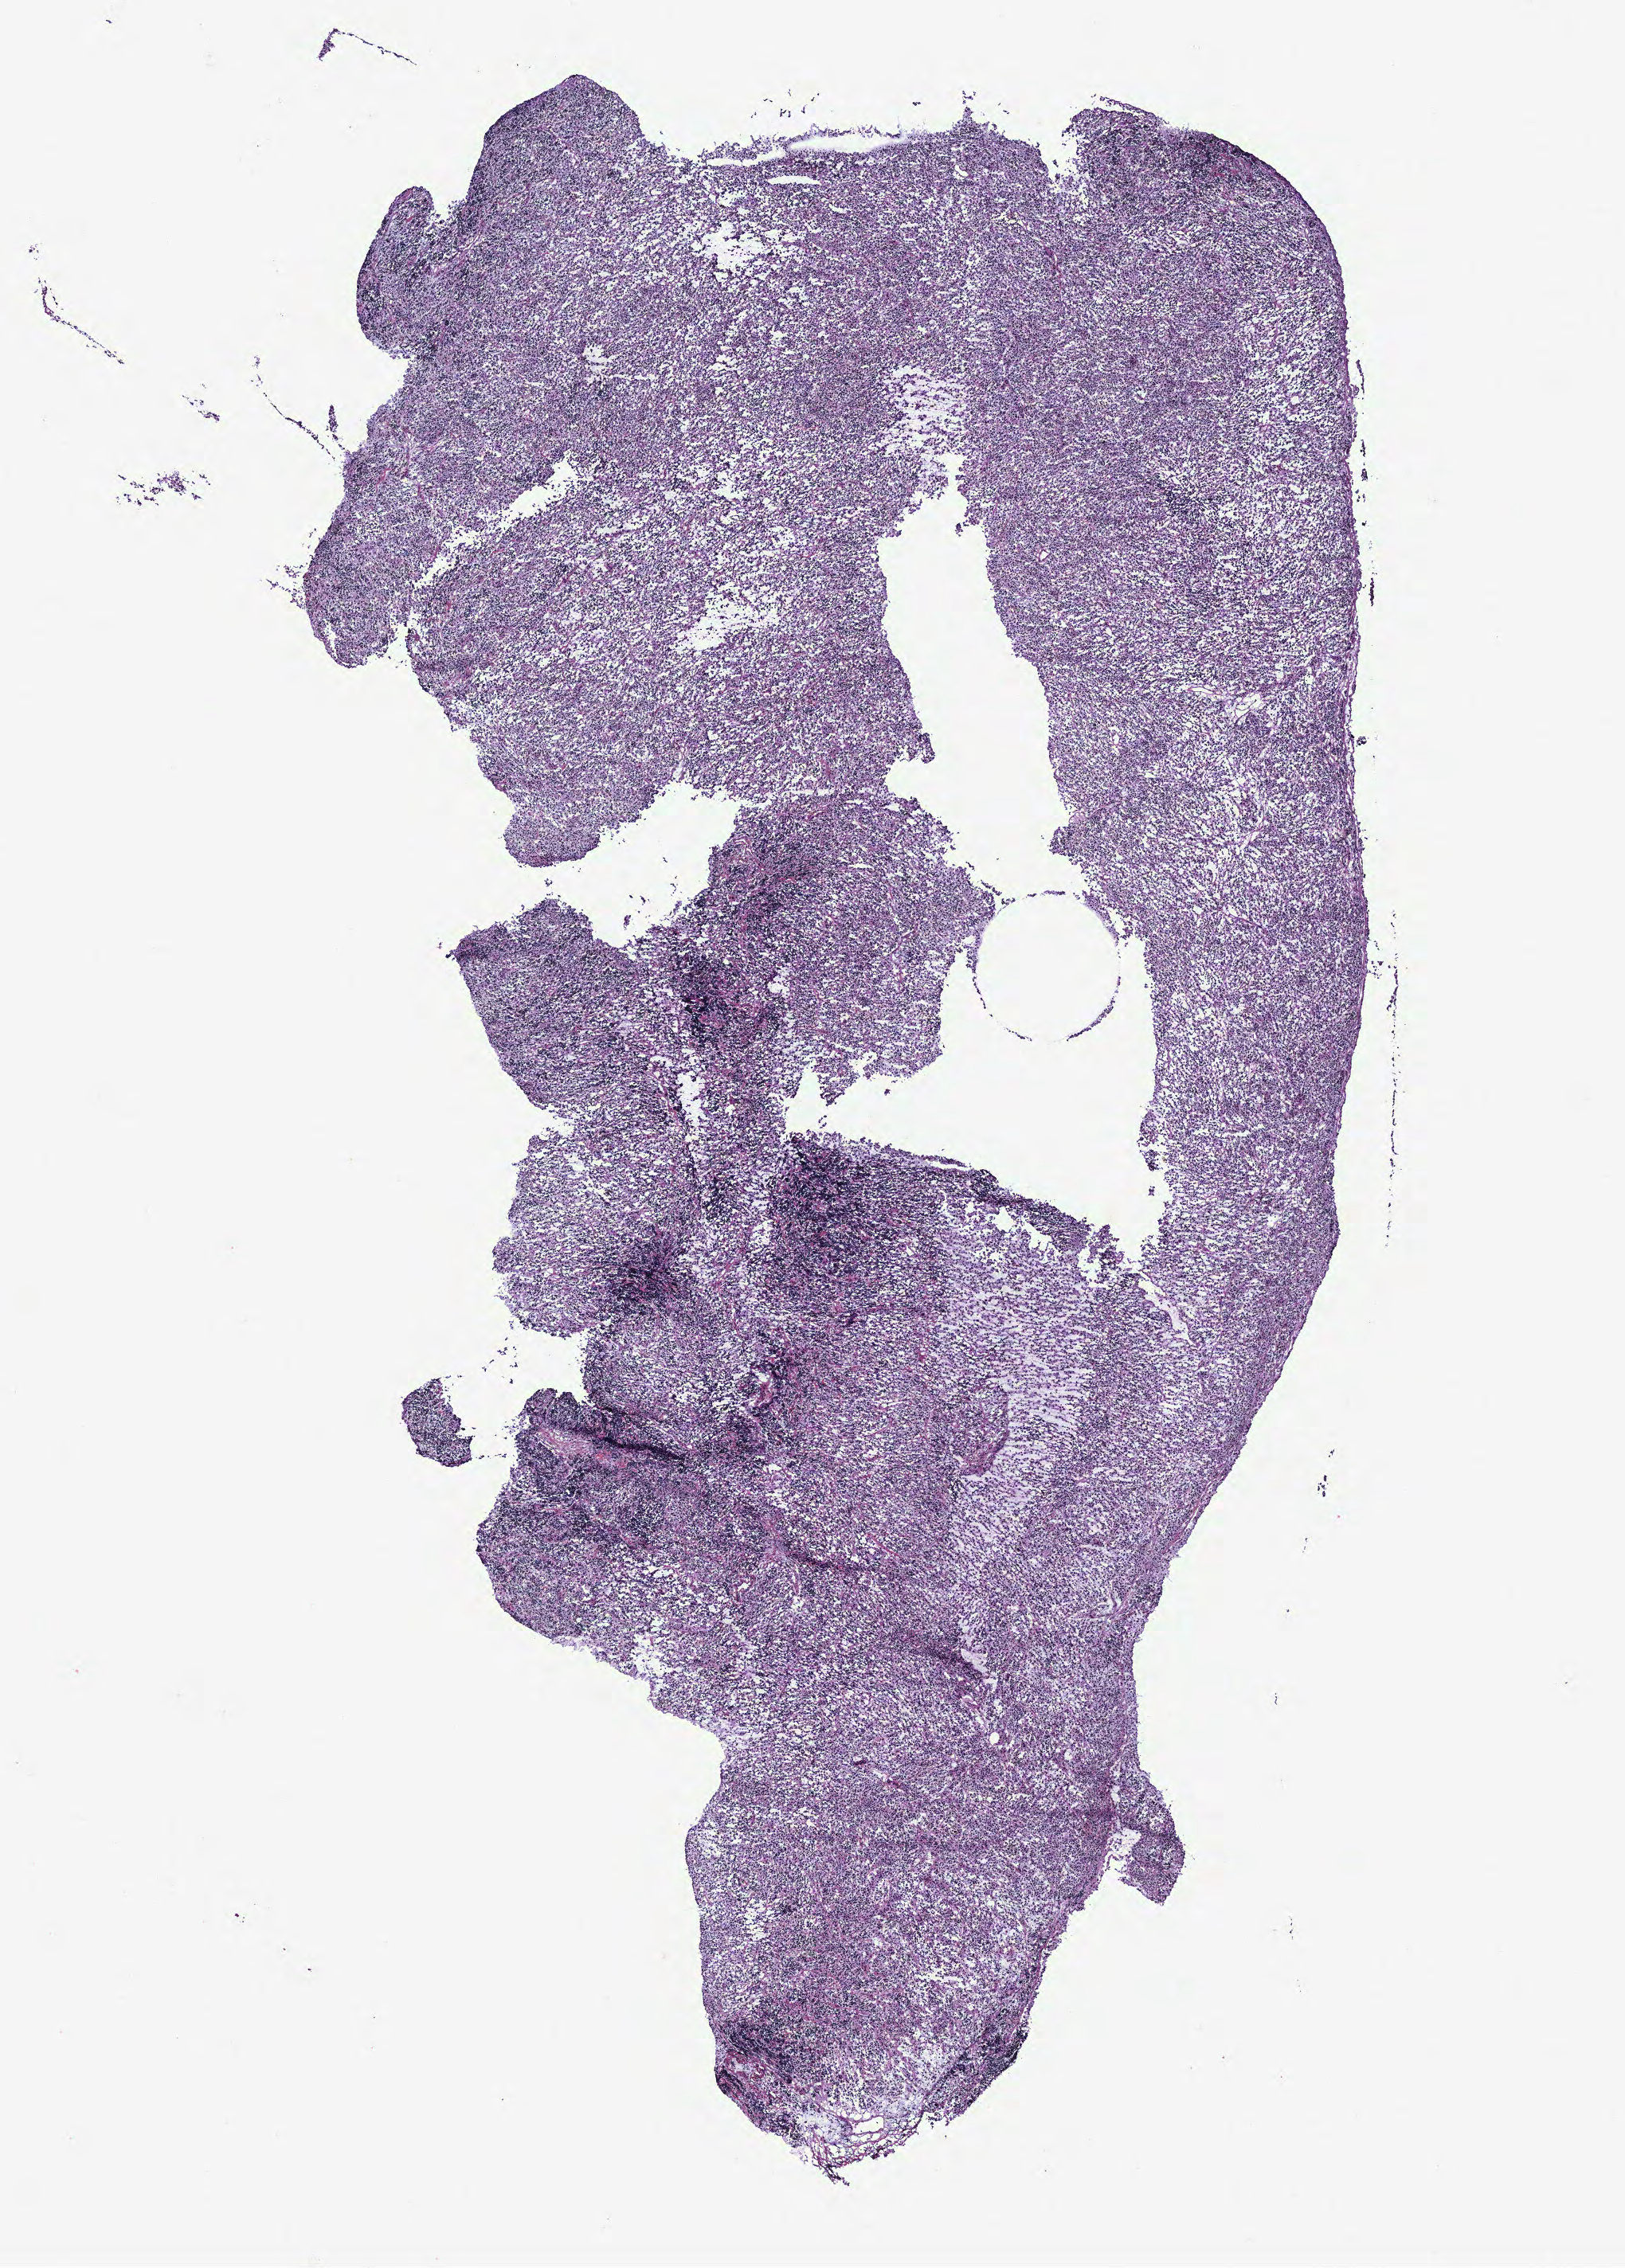
Hematoxylin and eosin (H&E) stained whole-slide image — low-resolution overview of the scanned area, about 8.2 x 11.4 mm (slide scanned at 40x). Ovary, tumour tissue. Patient: female, age 65 years.
Histologic diagnosis: Serous adenocarcinoma, NOS. Primary tumour site (as recorded): ovary.